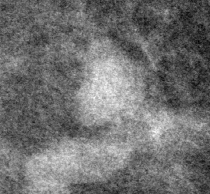
Crop from a digitized film mammogram around one marked abnormality, left breast, MLO view.
Mass, shape lymph node, margins circumscribed; BI-RADS assessment category 2; benign without callback (not worked up further).